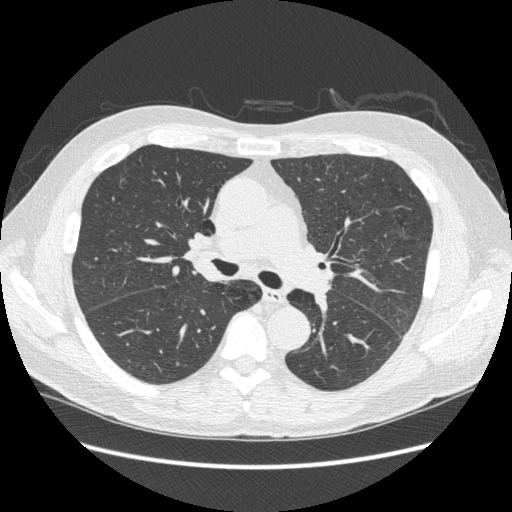
Axial slice from a low-dose chest CT screening exam; third annual screen; lung window (W 1500 / L -600 HU); 1.25 mm slice thickness; standard (soft-tissue) reconstruction kernel (STANDARD); slice 108 of 258 in the series; 512 × 512 image matrix. Male, age 59 years at enrolment.
Lesion marked by an expert reader, box from (x=180, y=225) to (x=231, y=266) px. The screening reader recorded 2 non-calcified nodules or masses ≥4 mm on this exam; which of them this box marks is not recorded. Official screen result: negative screen, minor abnormalities not suspicious for lung cancer.